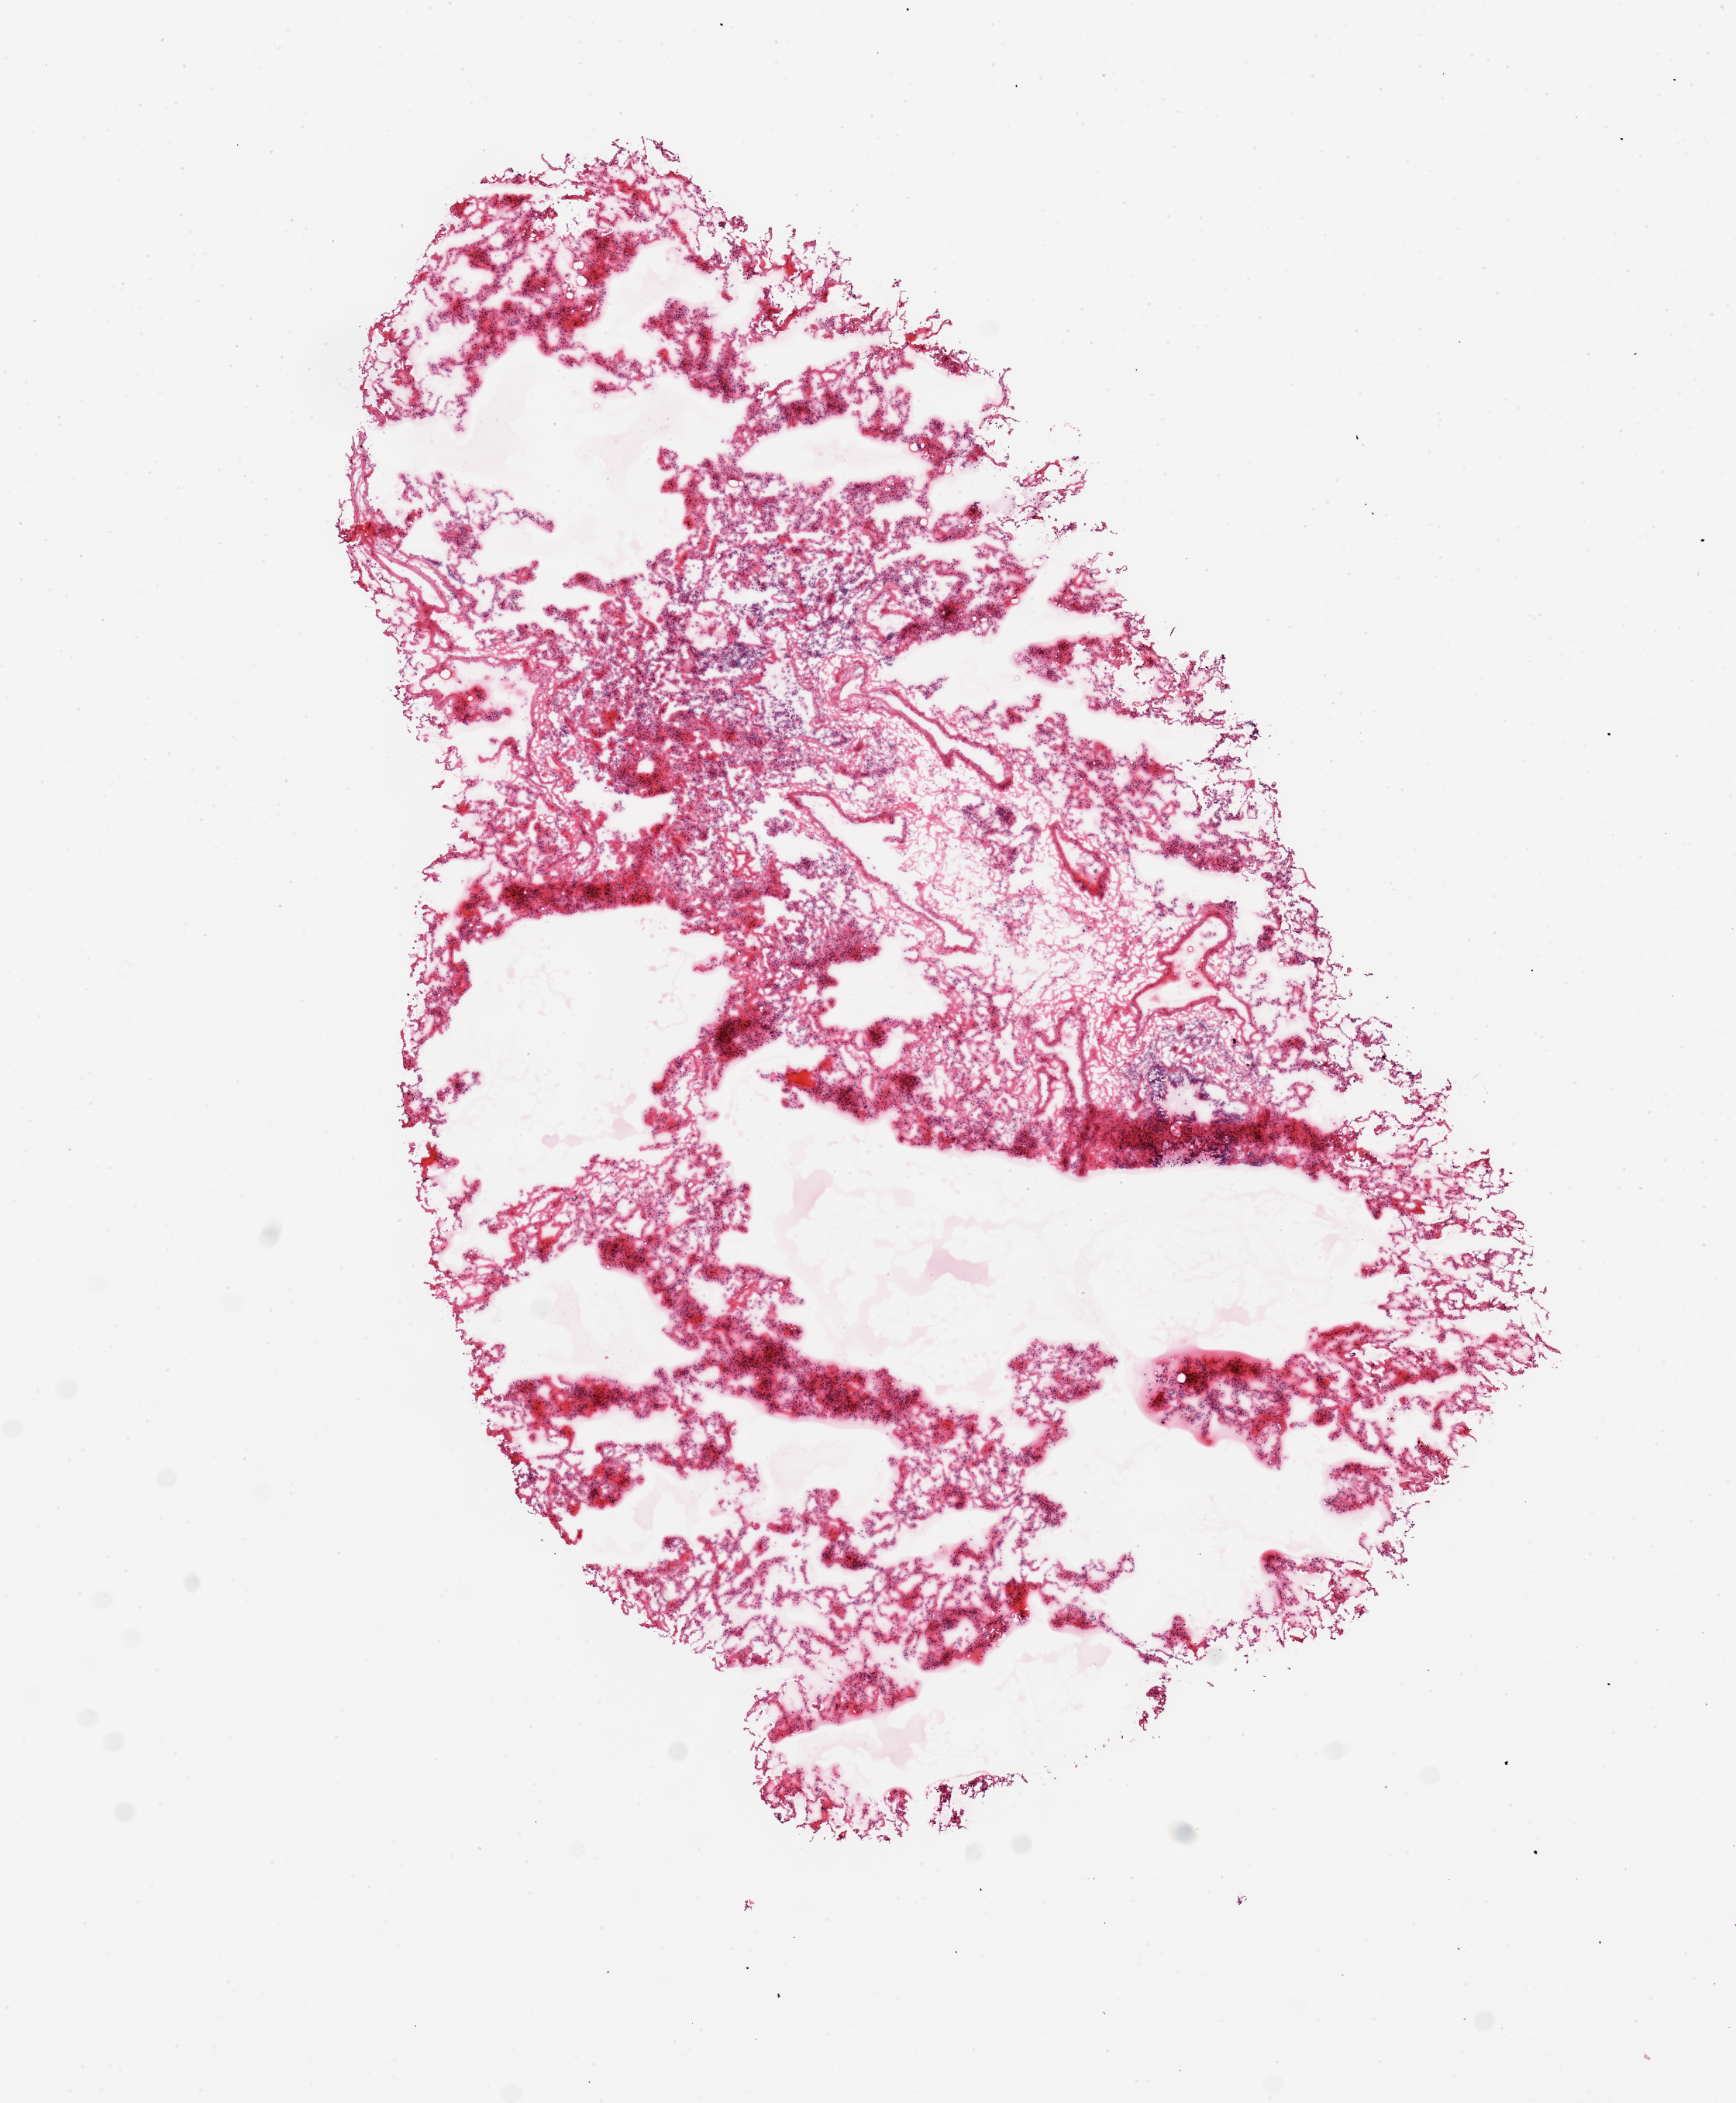
Whole-slide image, haematoxylin and eosin stain, whole scanned area (about 8.9 x 10.7 mm, from a 20x scan) shown as a low-resolution overview; frozen section (dry ice); section of lung (target tissue); tissue donor sample. Female donor.
- reviewer comment on this tissue sample: 1 piece